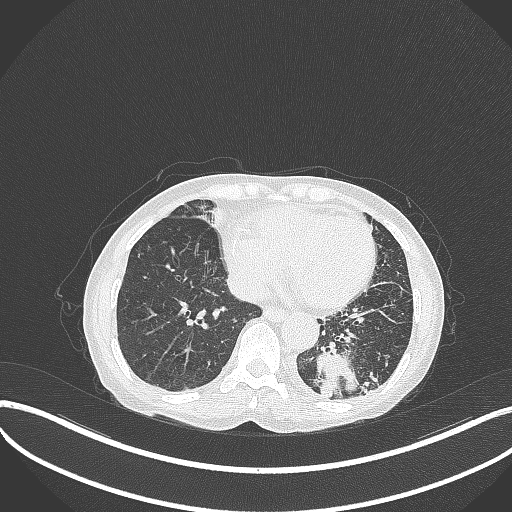
Chest CT, one axial slice; position 91 of 370 along the scan axis; lung window (W 1500 / L -600 HU); 1 mm slice thickness; 512 × 512 image matrix. Patient: female, 78 years. From the clinical record (not read from this slice): clinical TNM (as recorded): T3 N0 M1.
Structures marked on this image (rectangle marked by the reading radiologist):
- lung tumour (recorded histology: squamous cell carcinoma): bounding box (x1, y1, x2, y2) in pixels: (314, 343, 362, 405)